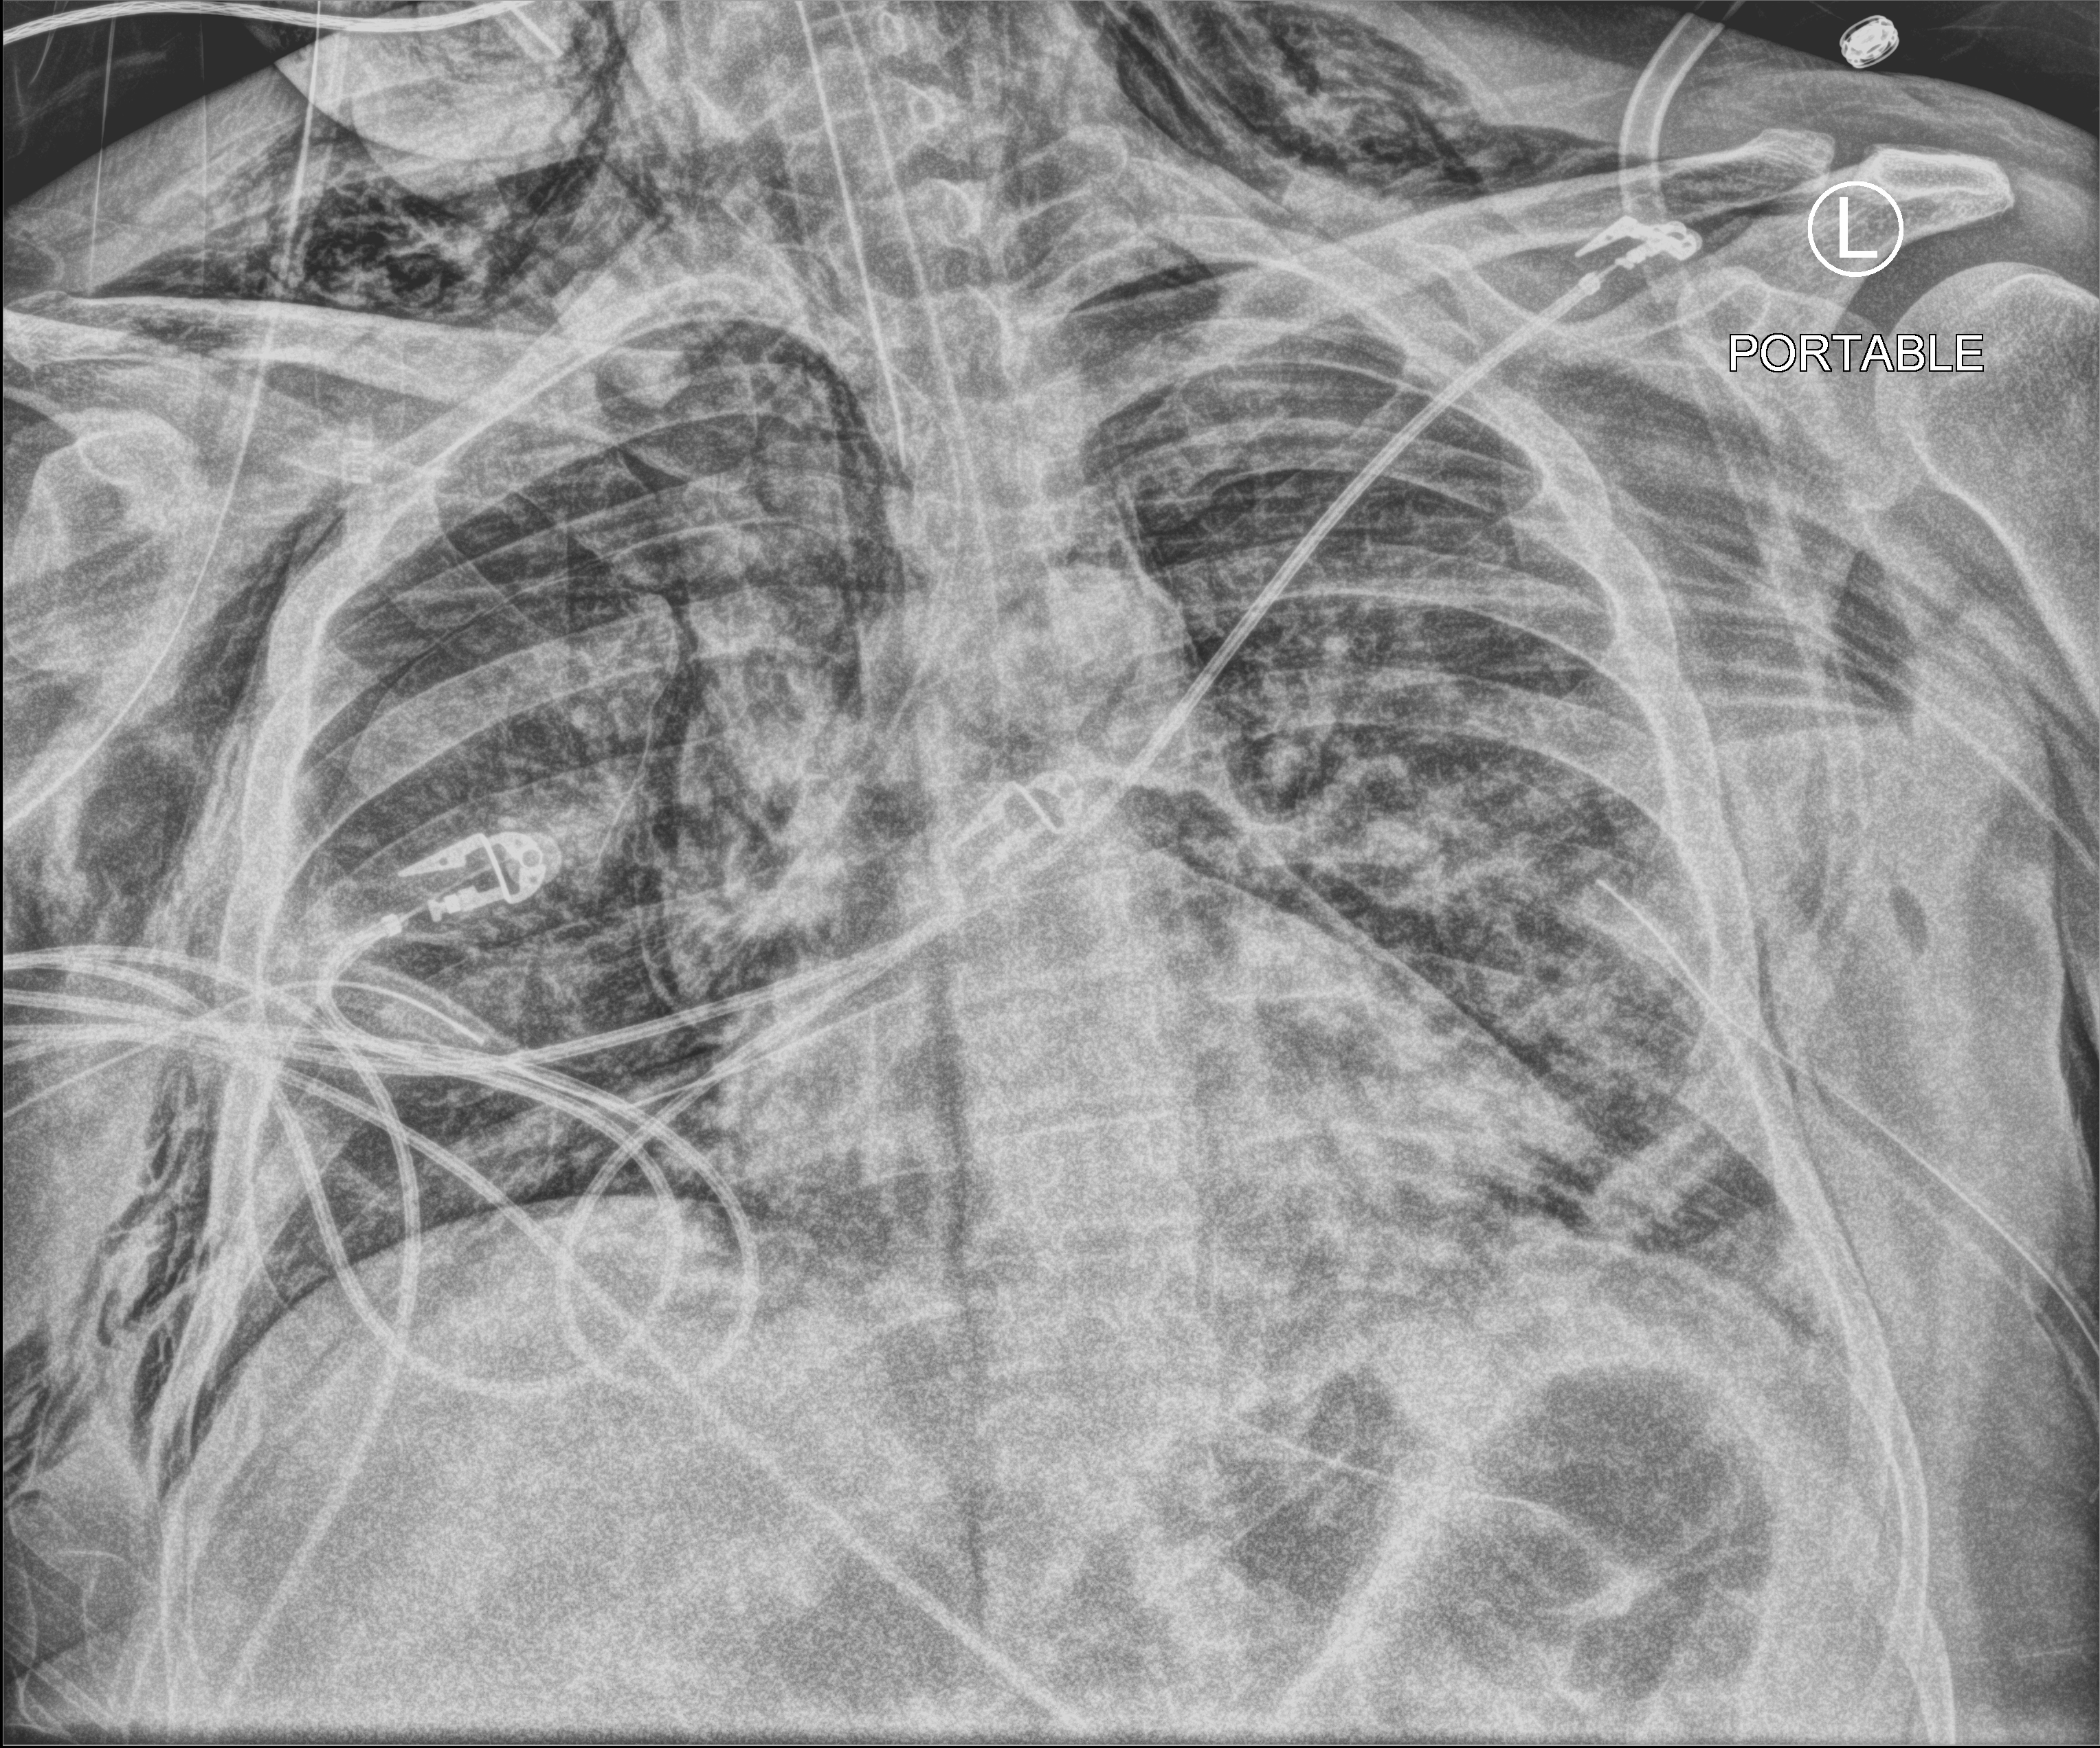
Bedside chest radiograph (computed radiography); anteroposterior (AP) projection. Male patient hospitalised with COVID-19, age 18–59 years.
Hospital-stay facts (about this admission, not read from this image; timing relative to this image not recorded): admitted to intensive care during this hospital stay: yes; COPD (admission record): no.